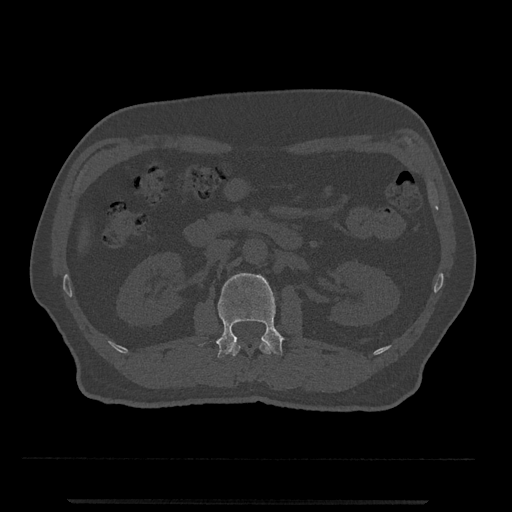
CT including the spine, one axial slice; slice 285 of 797 in the series (ordered by position); reconstruction kernel Br40s/3; 120 kVp; bone window (W 1800 / L 400 HU); 0.5 mm slice thickness; 512 × 512 image matrix, field of view 419 × 419 mm. Male patient, age 63 years. Case-level facts recorded for this patient, not image findings: primary cancer: prostate.
Structures marked on this image (semi-automatic segmentation, software-assisted and operator-edited):
- L1 vertebra: bounding box (x1, y1, x2, y2) in pixels: (231, 340, 273, 356)
- L2 vertebra: (217, 273, 283, 358)